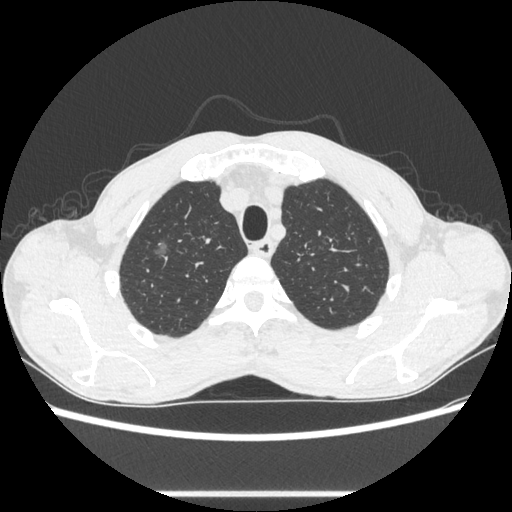
Chest CT, one axial slice; position 497 of 600 along the scan axis; lung window (W 1500 / L -600 HU); 0.62 mm slice thickness; 512 × 512 image matrix, field of view 357 × 357 mm. Male patient, age 54 years. From the clinical record (not read from this slice): clinical TNM (as recorded): T1a N0 M0.
Structures marked on this image (rectangle marked by the reading radiologist):
- lung tumour (recorded histology: adenocarcinoma): bounding box <148,236,177,262> (left, top, right, bottom; pixels)